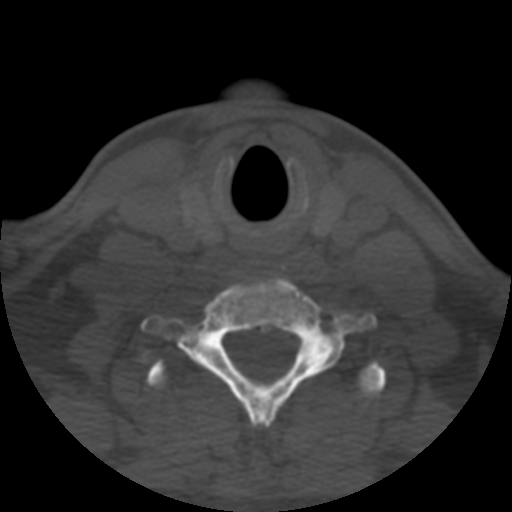
CT including the spine, one axial slice; slice 462 of 508 in the series (ordered by position); 120 kVp; bone window (W 1800 / L 400 HU); 1.25 mm slice thickness; 512 × 512 image matrix, field of view 160 × 160 mm. Patient age 57 years. Case-level facts recorded for this patient, not image findings: primary cancer: prostate.
Annotated regions visible in this slice (semi-automatically segmented with operator editing):
- T1 vertebra: bounding box [x1, y1, x2, y2] px = [146, 360, 386, 397]